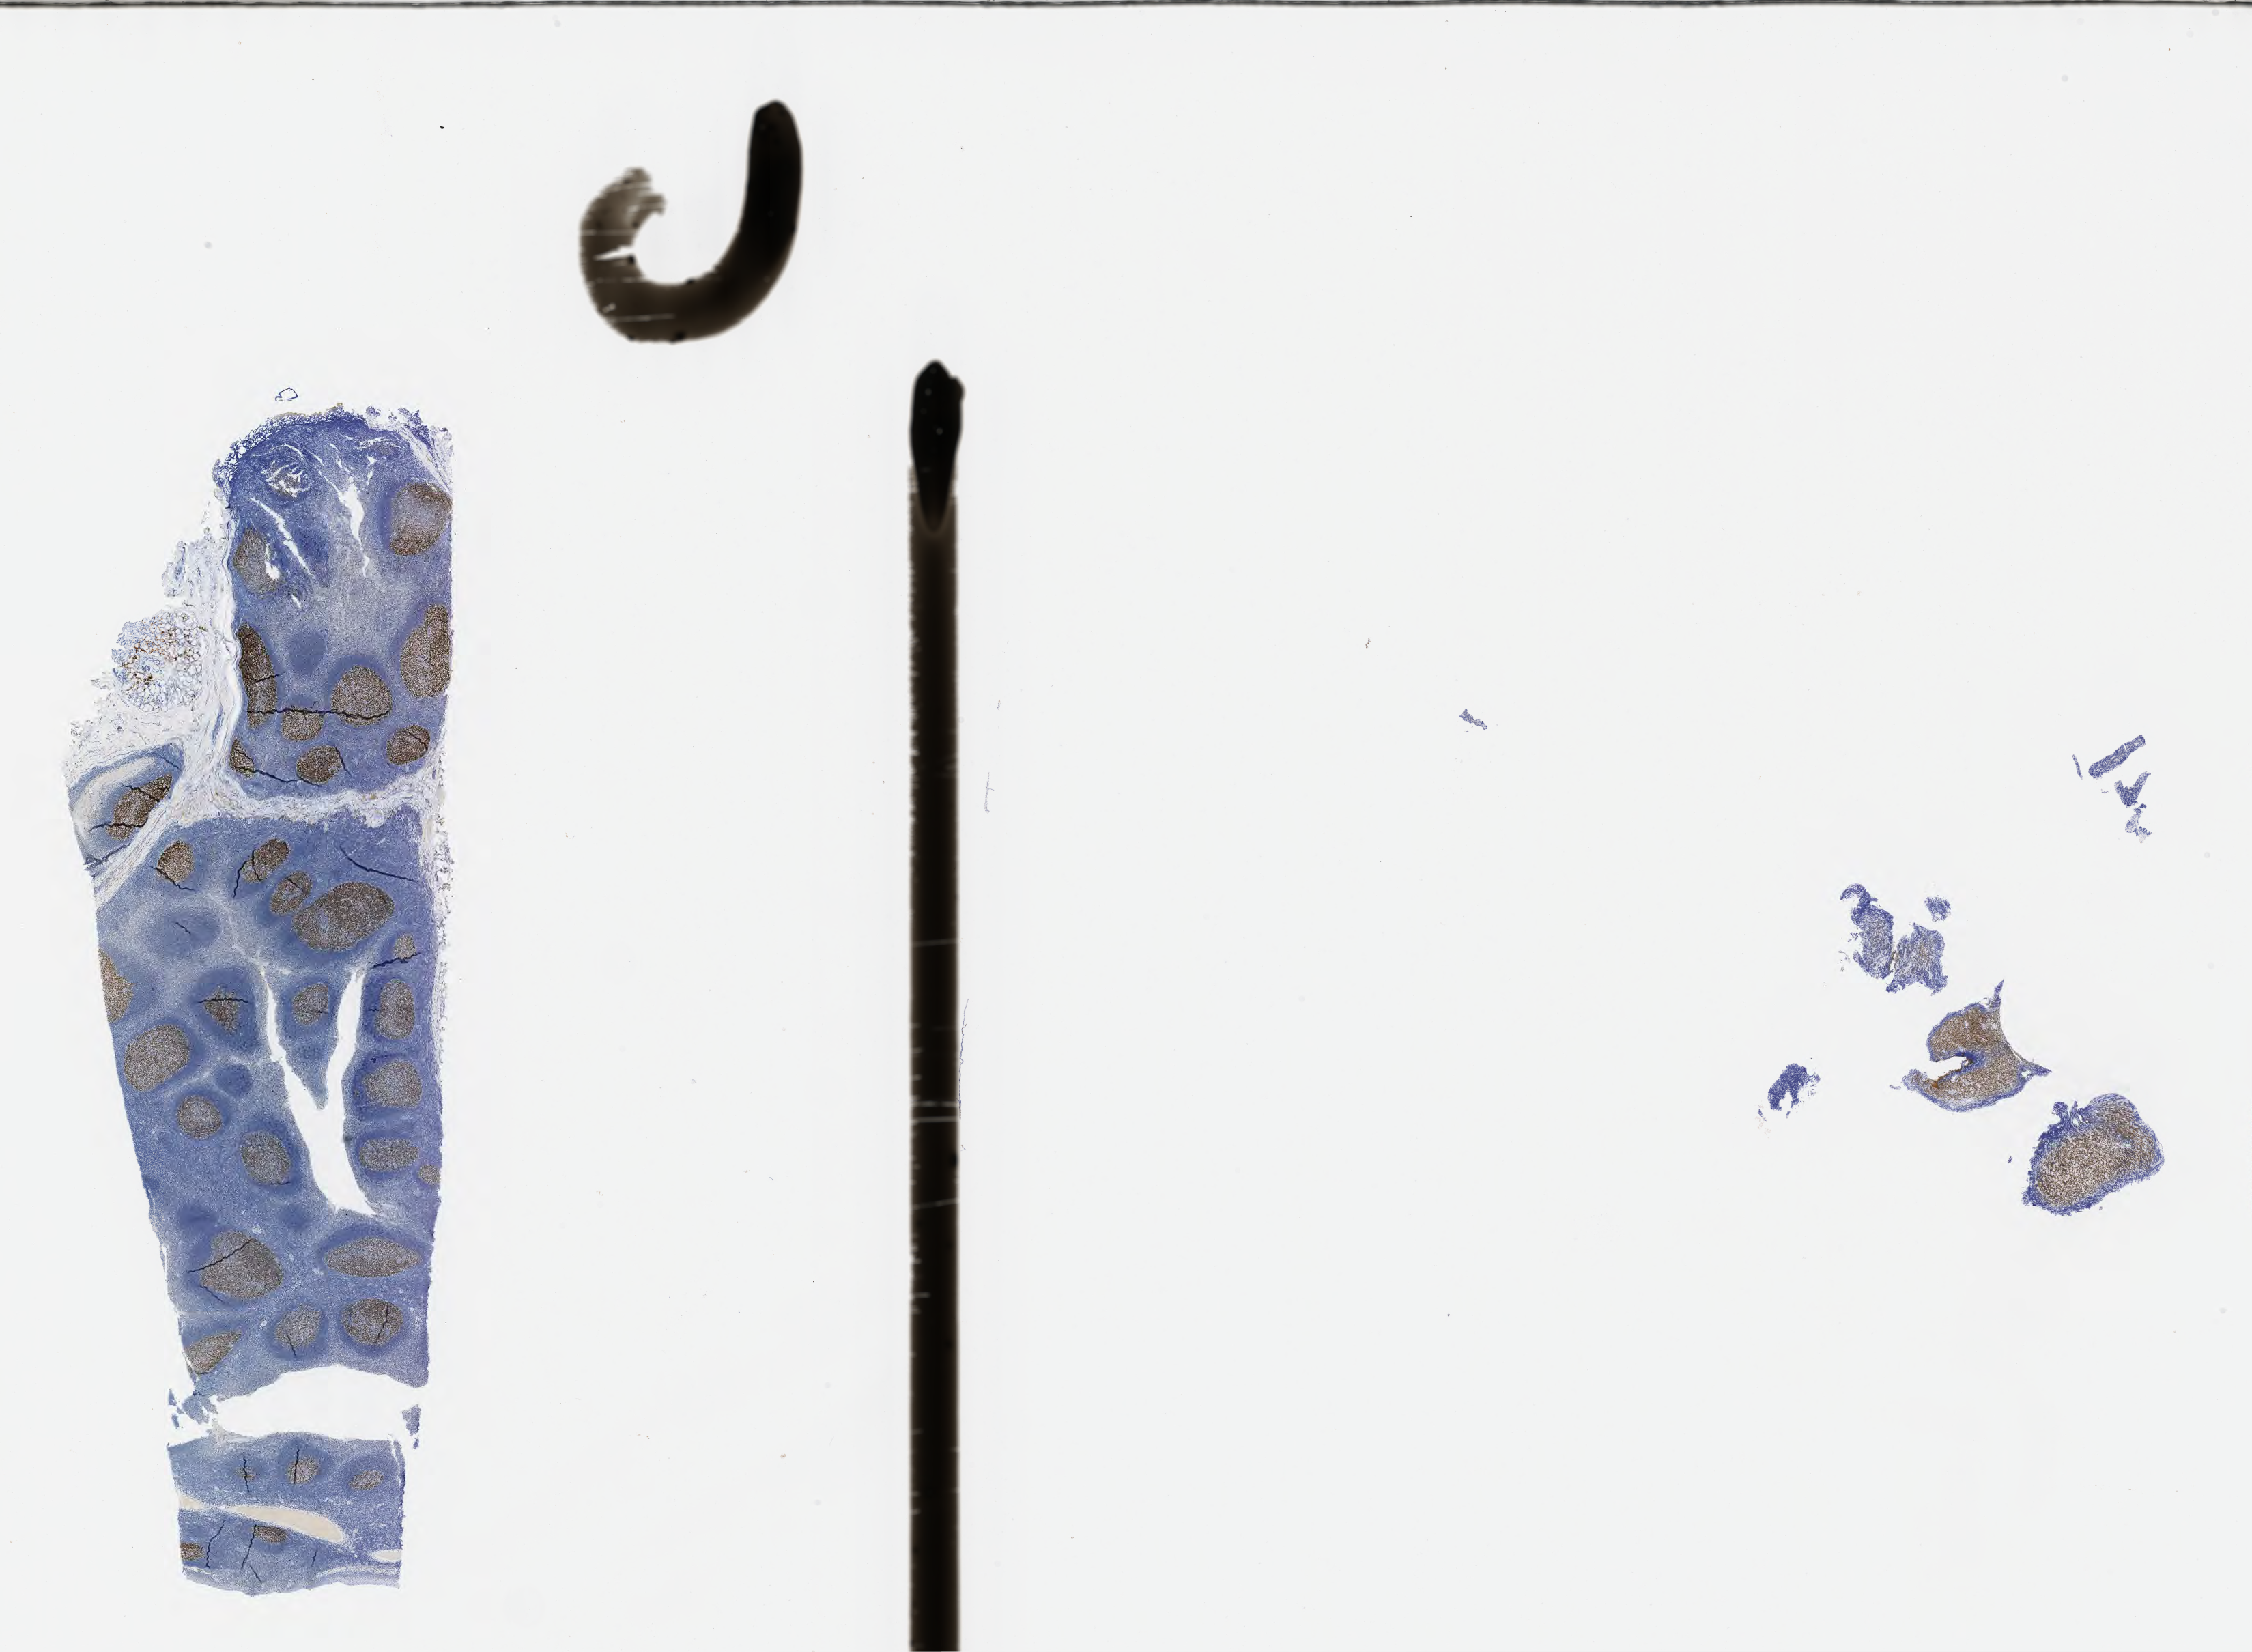
Immunohistochemistry (IHC) whole-slide image stained for BCL6, whole scanned area (about 26.7 x 19.6 mm) shown as a low-resolution overview, tumor tissue, site: small intestine. Female patient, age 47 years.
- diagnosis: Burkitt lymphoma, NOS